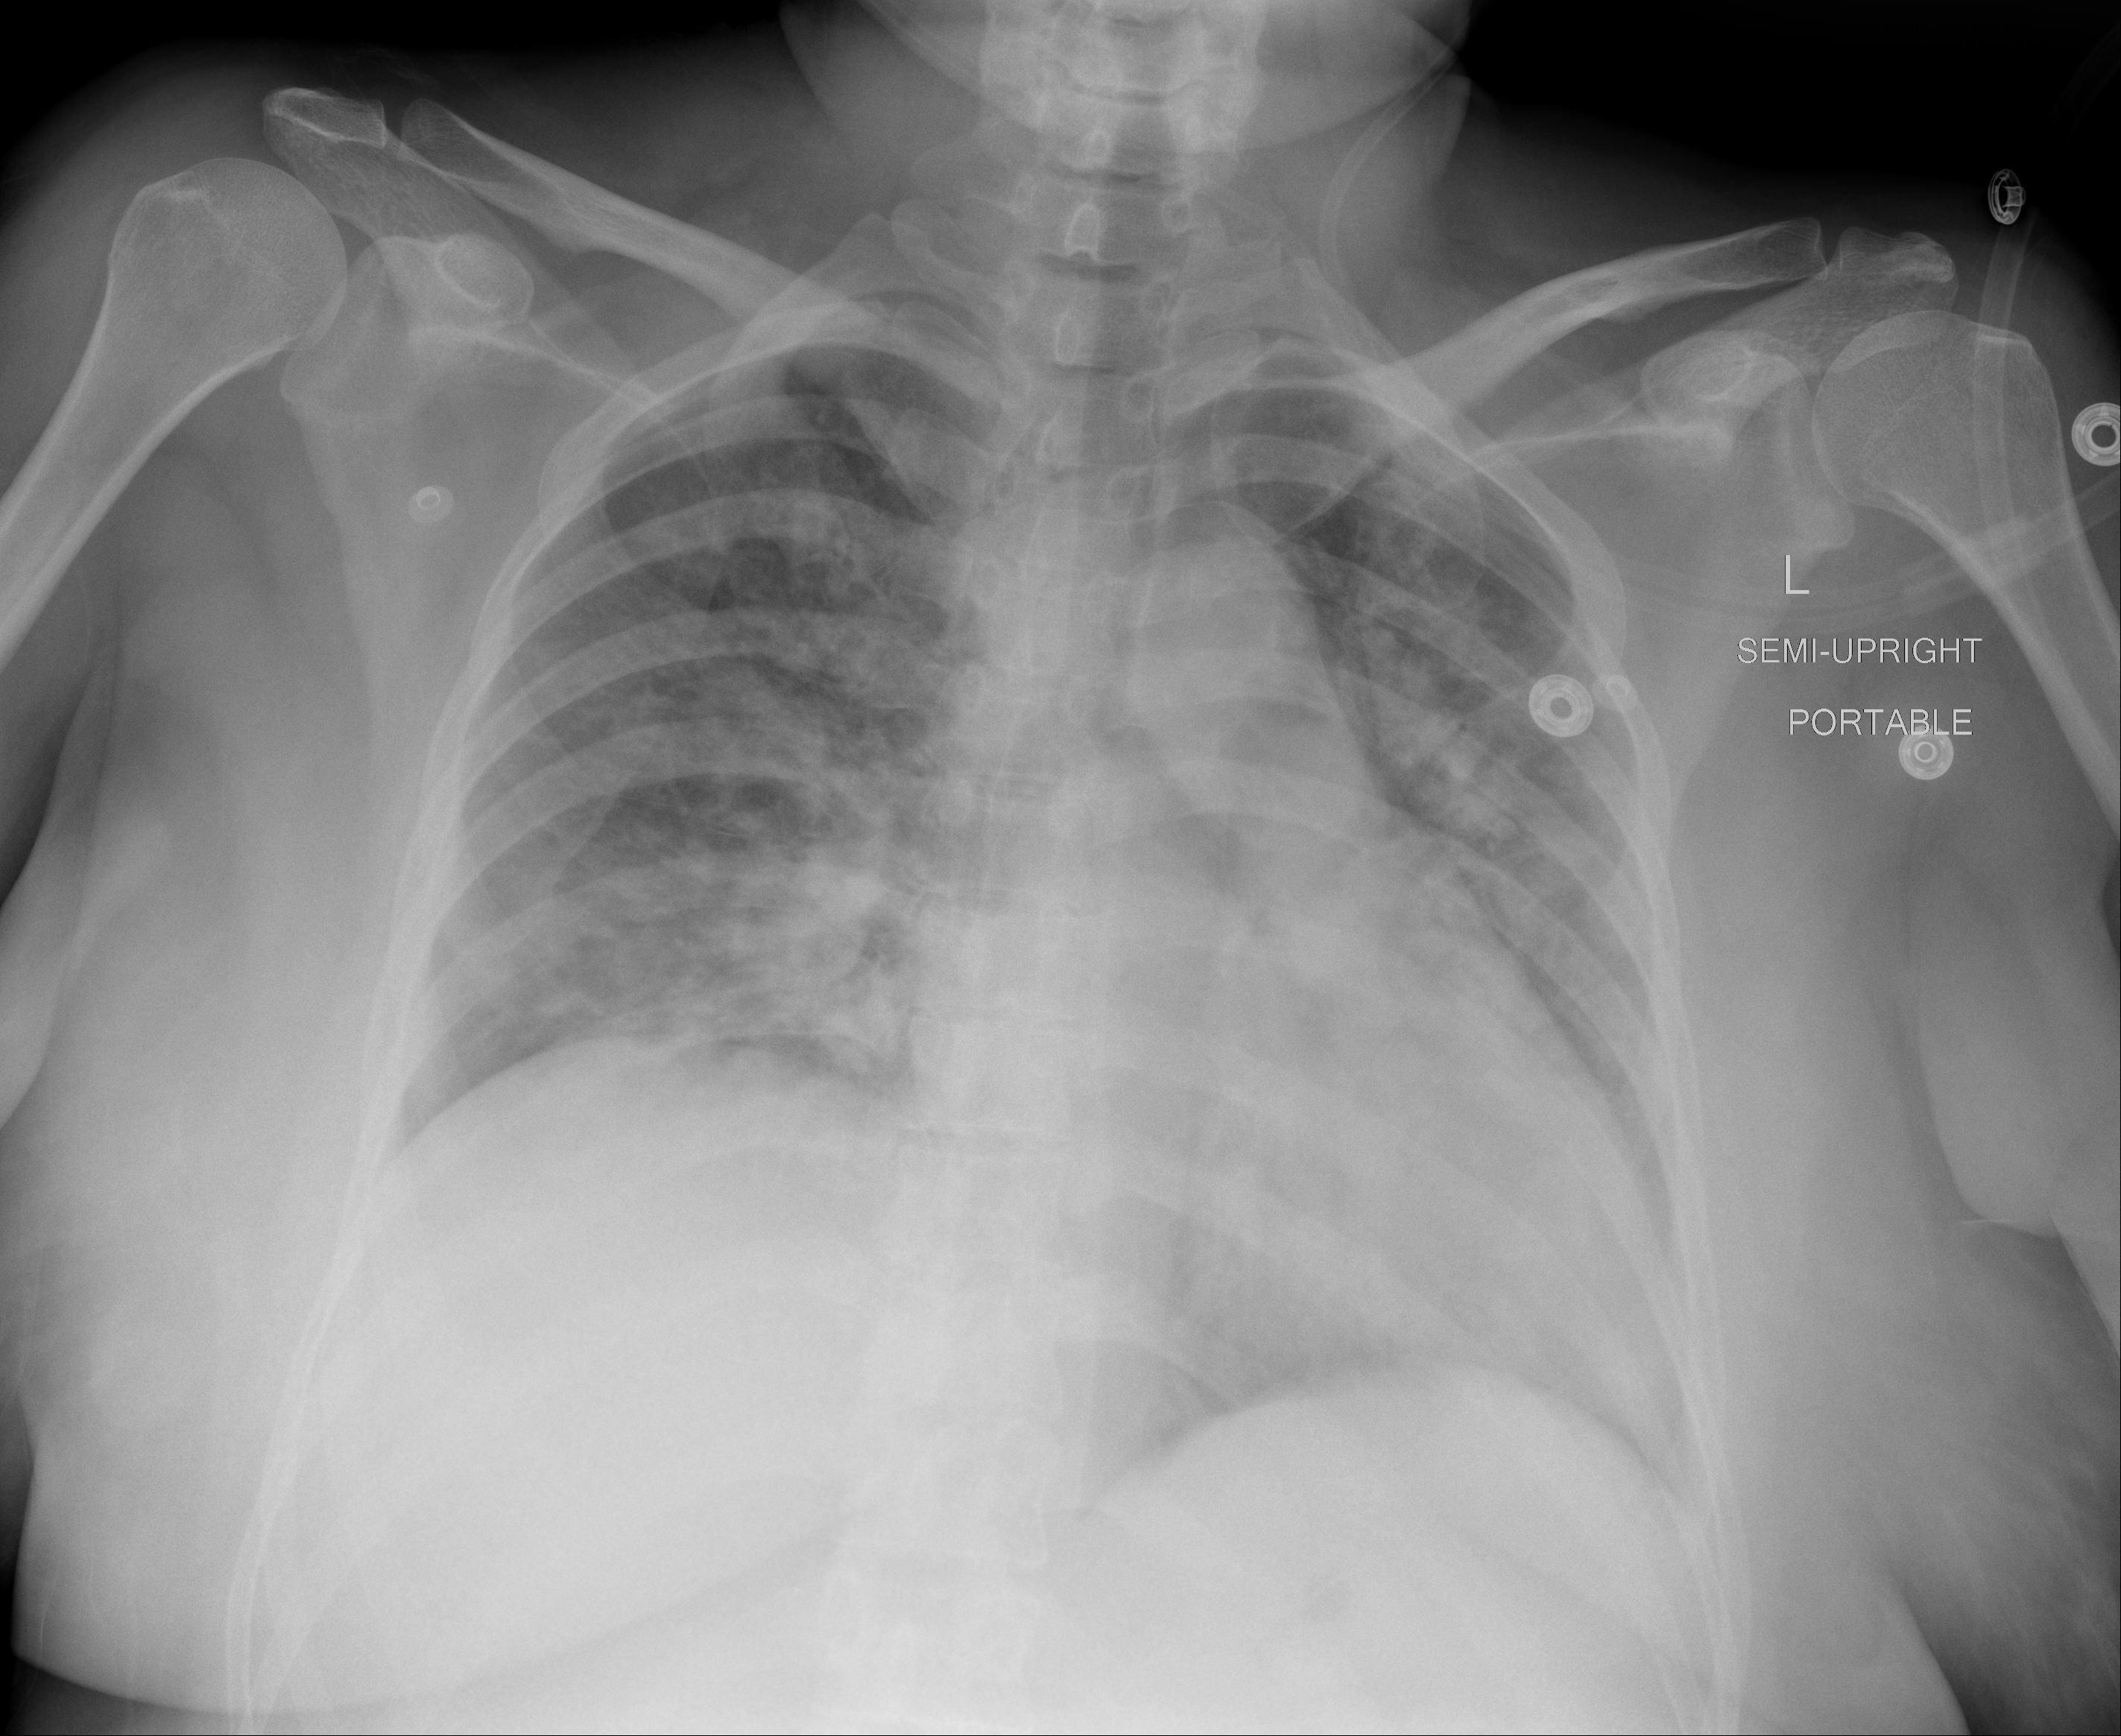
Chest X-ray (portable), AP projection. Female patient, age 39 years; imaged 0 days after the COVID-19 diagnosis.
Radiologist's key findings for this exam: Diffusely distributed throughout the lungs are areas of consolidation and ground-glass changes.